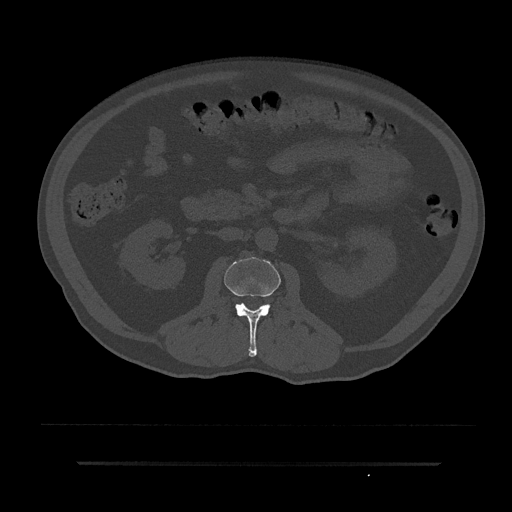
CT including the spine, one axial slice; slice 64 of 797 in the series (ordered by position); reconstruction kernel Br40s/3; bone window (W 1800 / L 400 HU); 0.5 mm slice thickness; 512 × 512 image matrix, field of view 464 × 464 mm. Male patient, age 59 years. Case-level facts recorded for this patient, not image findings: primary cancer: bile ducts.
Structures marked on this image (semi-automatically segmented with operator editing):
- L2 vertebra: bounding box [x1, y1, x2, y2] px = [224, 257, 281, 357]